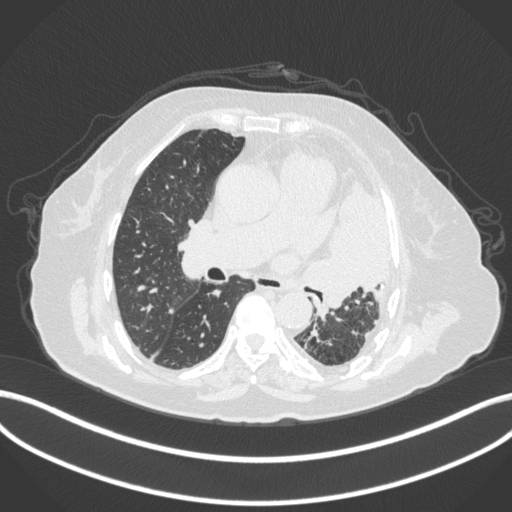
Chest CT, one axial slice; position 206 of 399 along the scan axis; lung window (W 1500 / L -600 HU); 1 mm slice thickness; 512 × 512 image matrix, field of view 400 × 400 mm. Female patient, age 75 years. From the clinical record (not read from this slice): clinical TNM (as recorded): T3 N3 M1.
Structures marked on this image (bounding box drawn by a radiologist):
- lung tumour (recorded histology: adenocarcinoma): box from (x=299, y=186) to (x=389, y=313) px